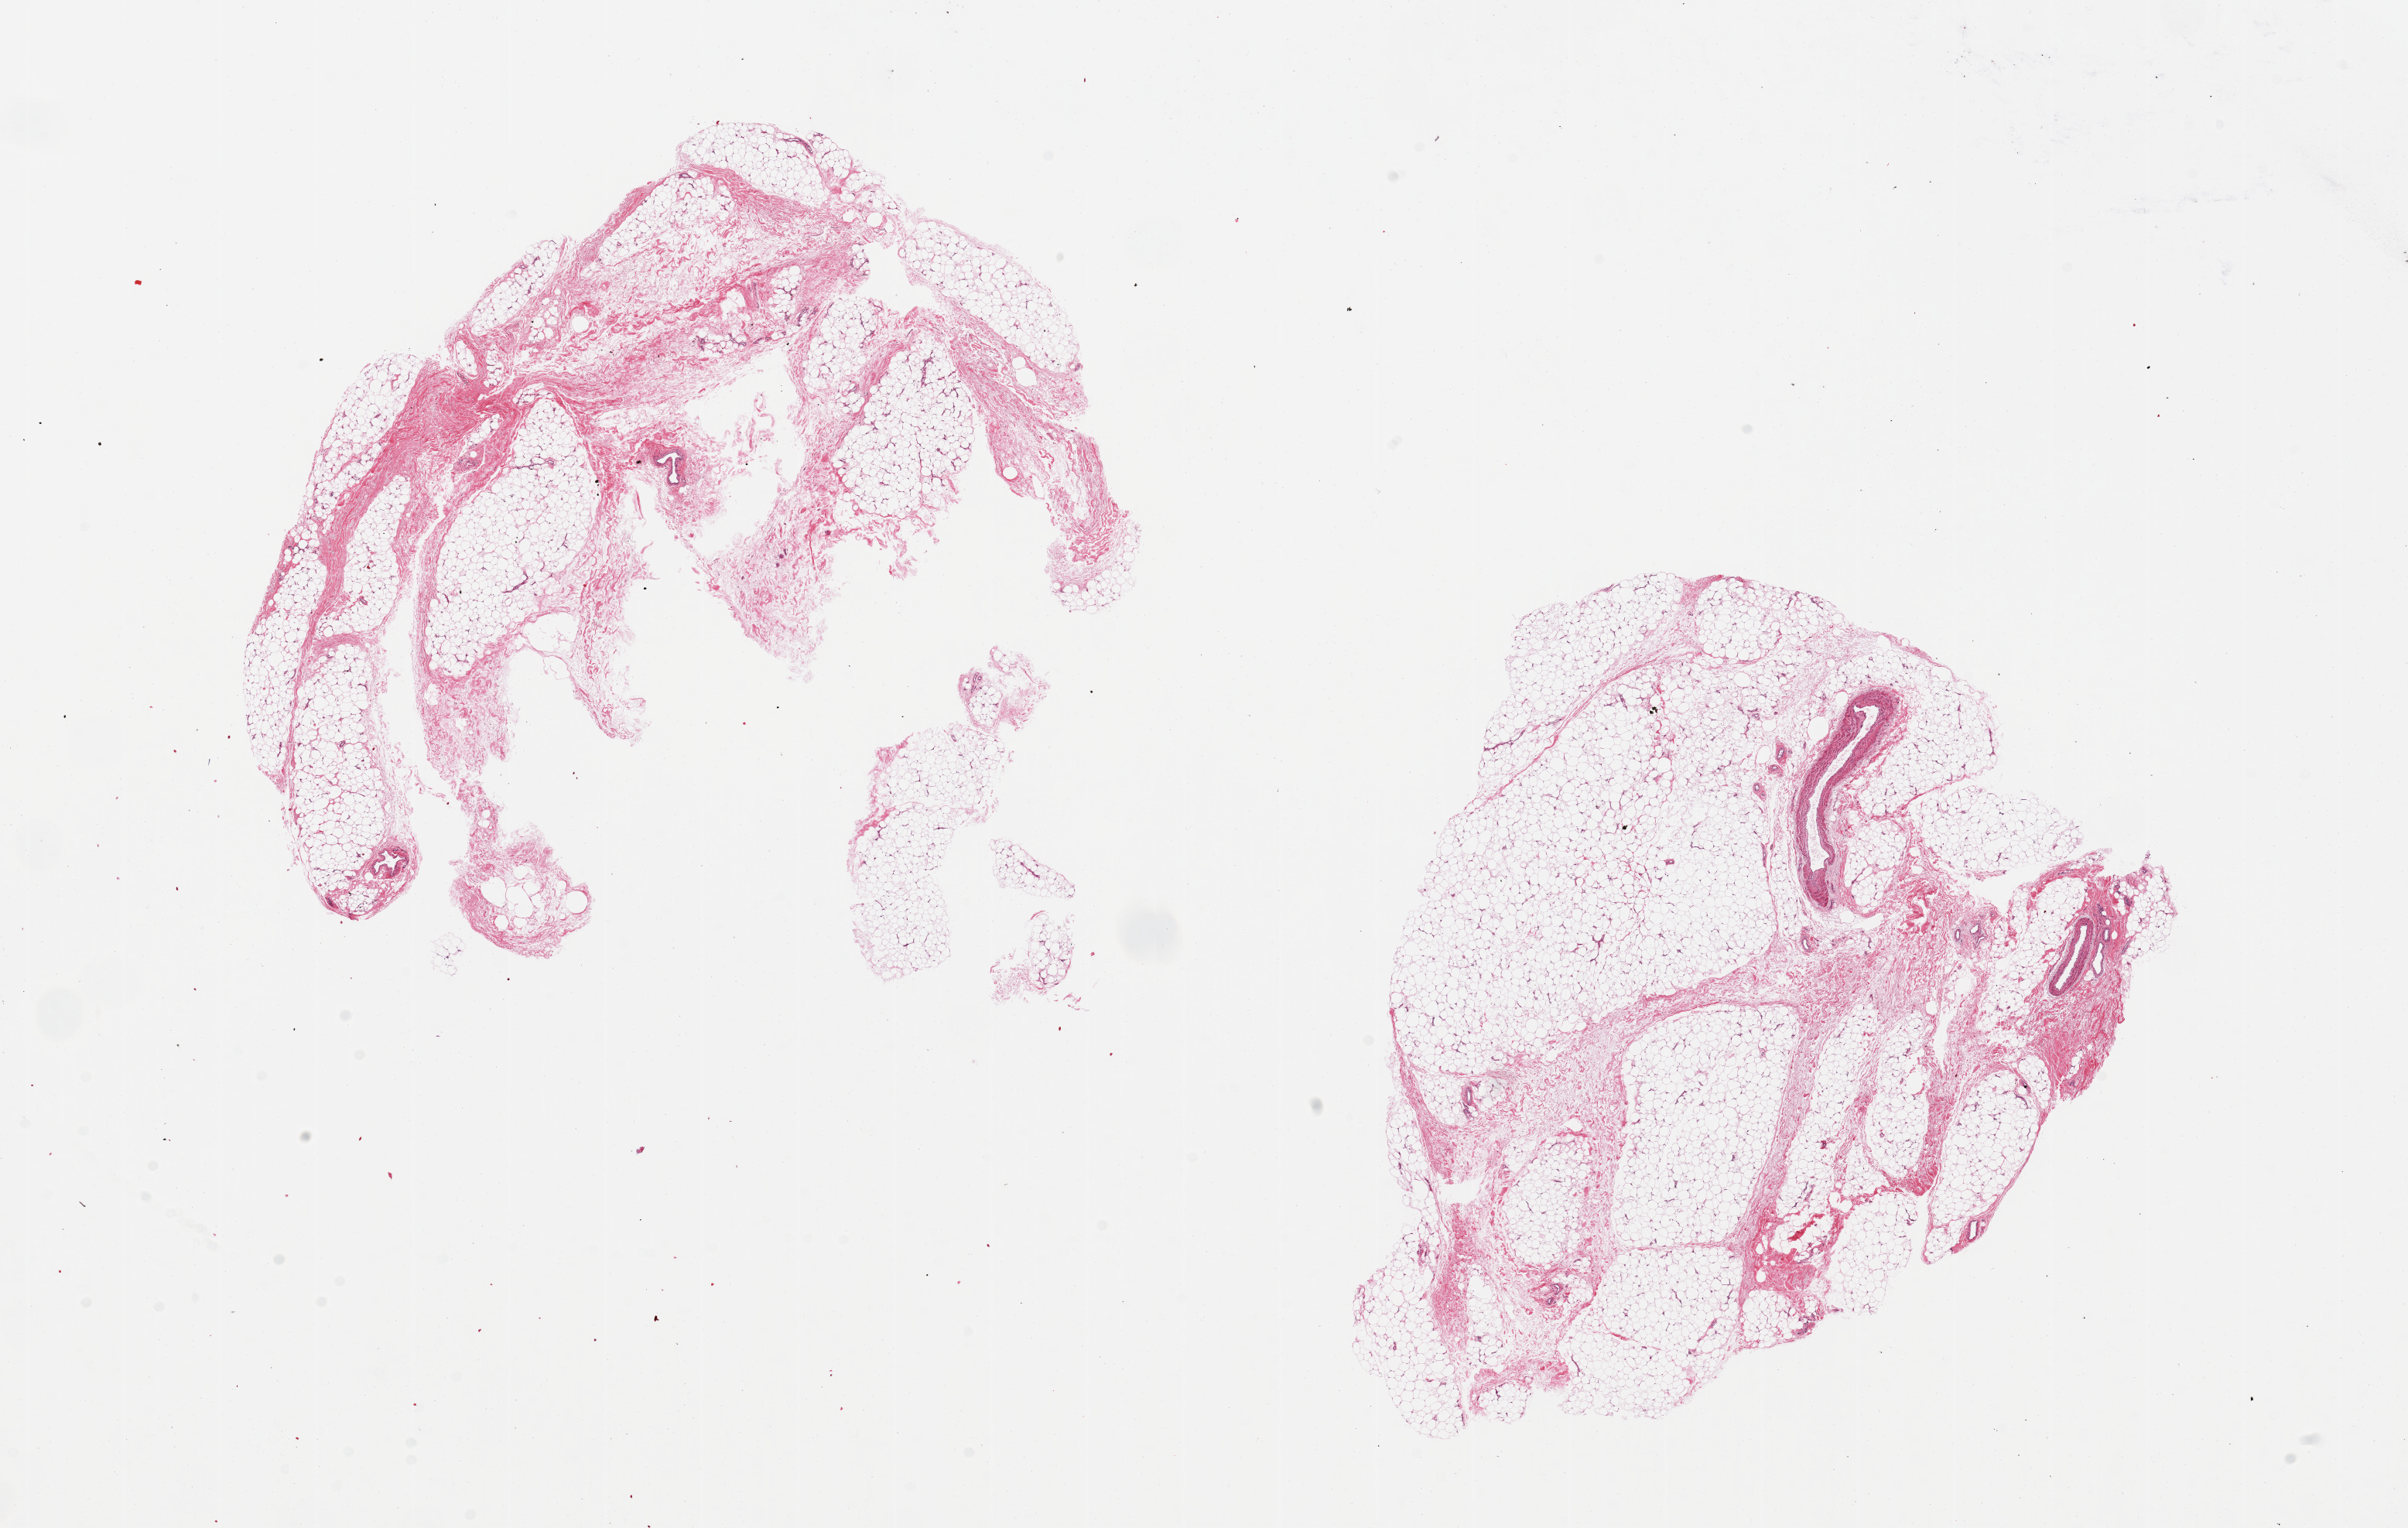
Whole-slide image, haematoxylin and eosin stain, a low-resolution overview of the entire scanned area, about 24.6 x 15.6 mm. PAXgene-fixed, paraffin-embedded tissue. Sampled site (target tissue): adipose tissue. Donor tissue sample.
Reviewer comment on this tissue sample: 2 pieces; 10% fibrovascular content.